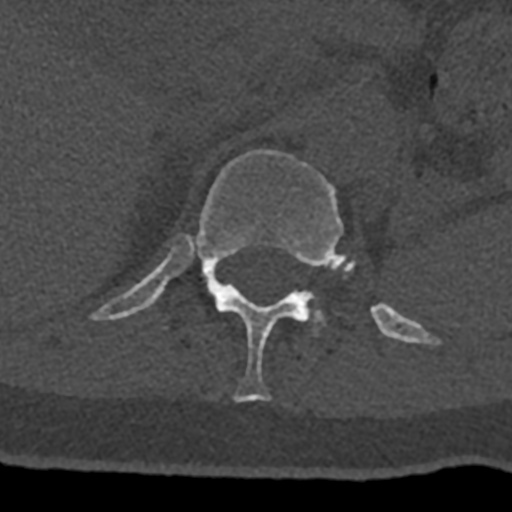
CT including the spine, one axial slice. Position 487 of 797 along the scan axis. Reconstruction kernel Br40s/3. Bone window (W 1800 / L 400 HU). 0.5 mm slice thickness. 512 × 512 image matrix, field of view 160 × 160 mm. Patient: male, 74 years. Case-level facts recorded for this patient, not image findings: primary cancer: renal.
Structures marked on this image (semi-automatically segmented with operator editing):
- L1 vertebra: bounding box [x1, y1, x2, y2] px = [307, 295, 325, 333]
- T12 vertebra: [91, 150, 432, 403]